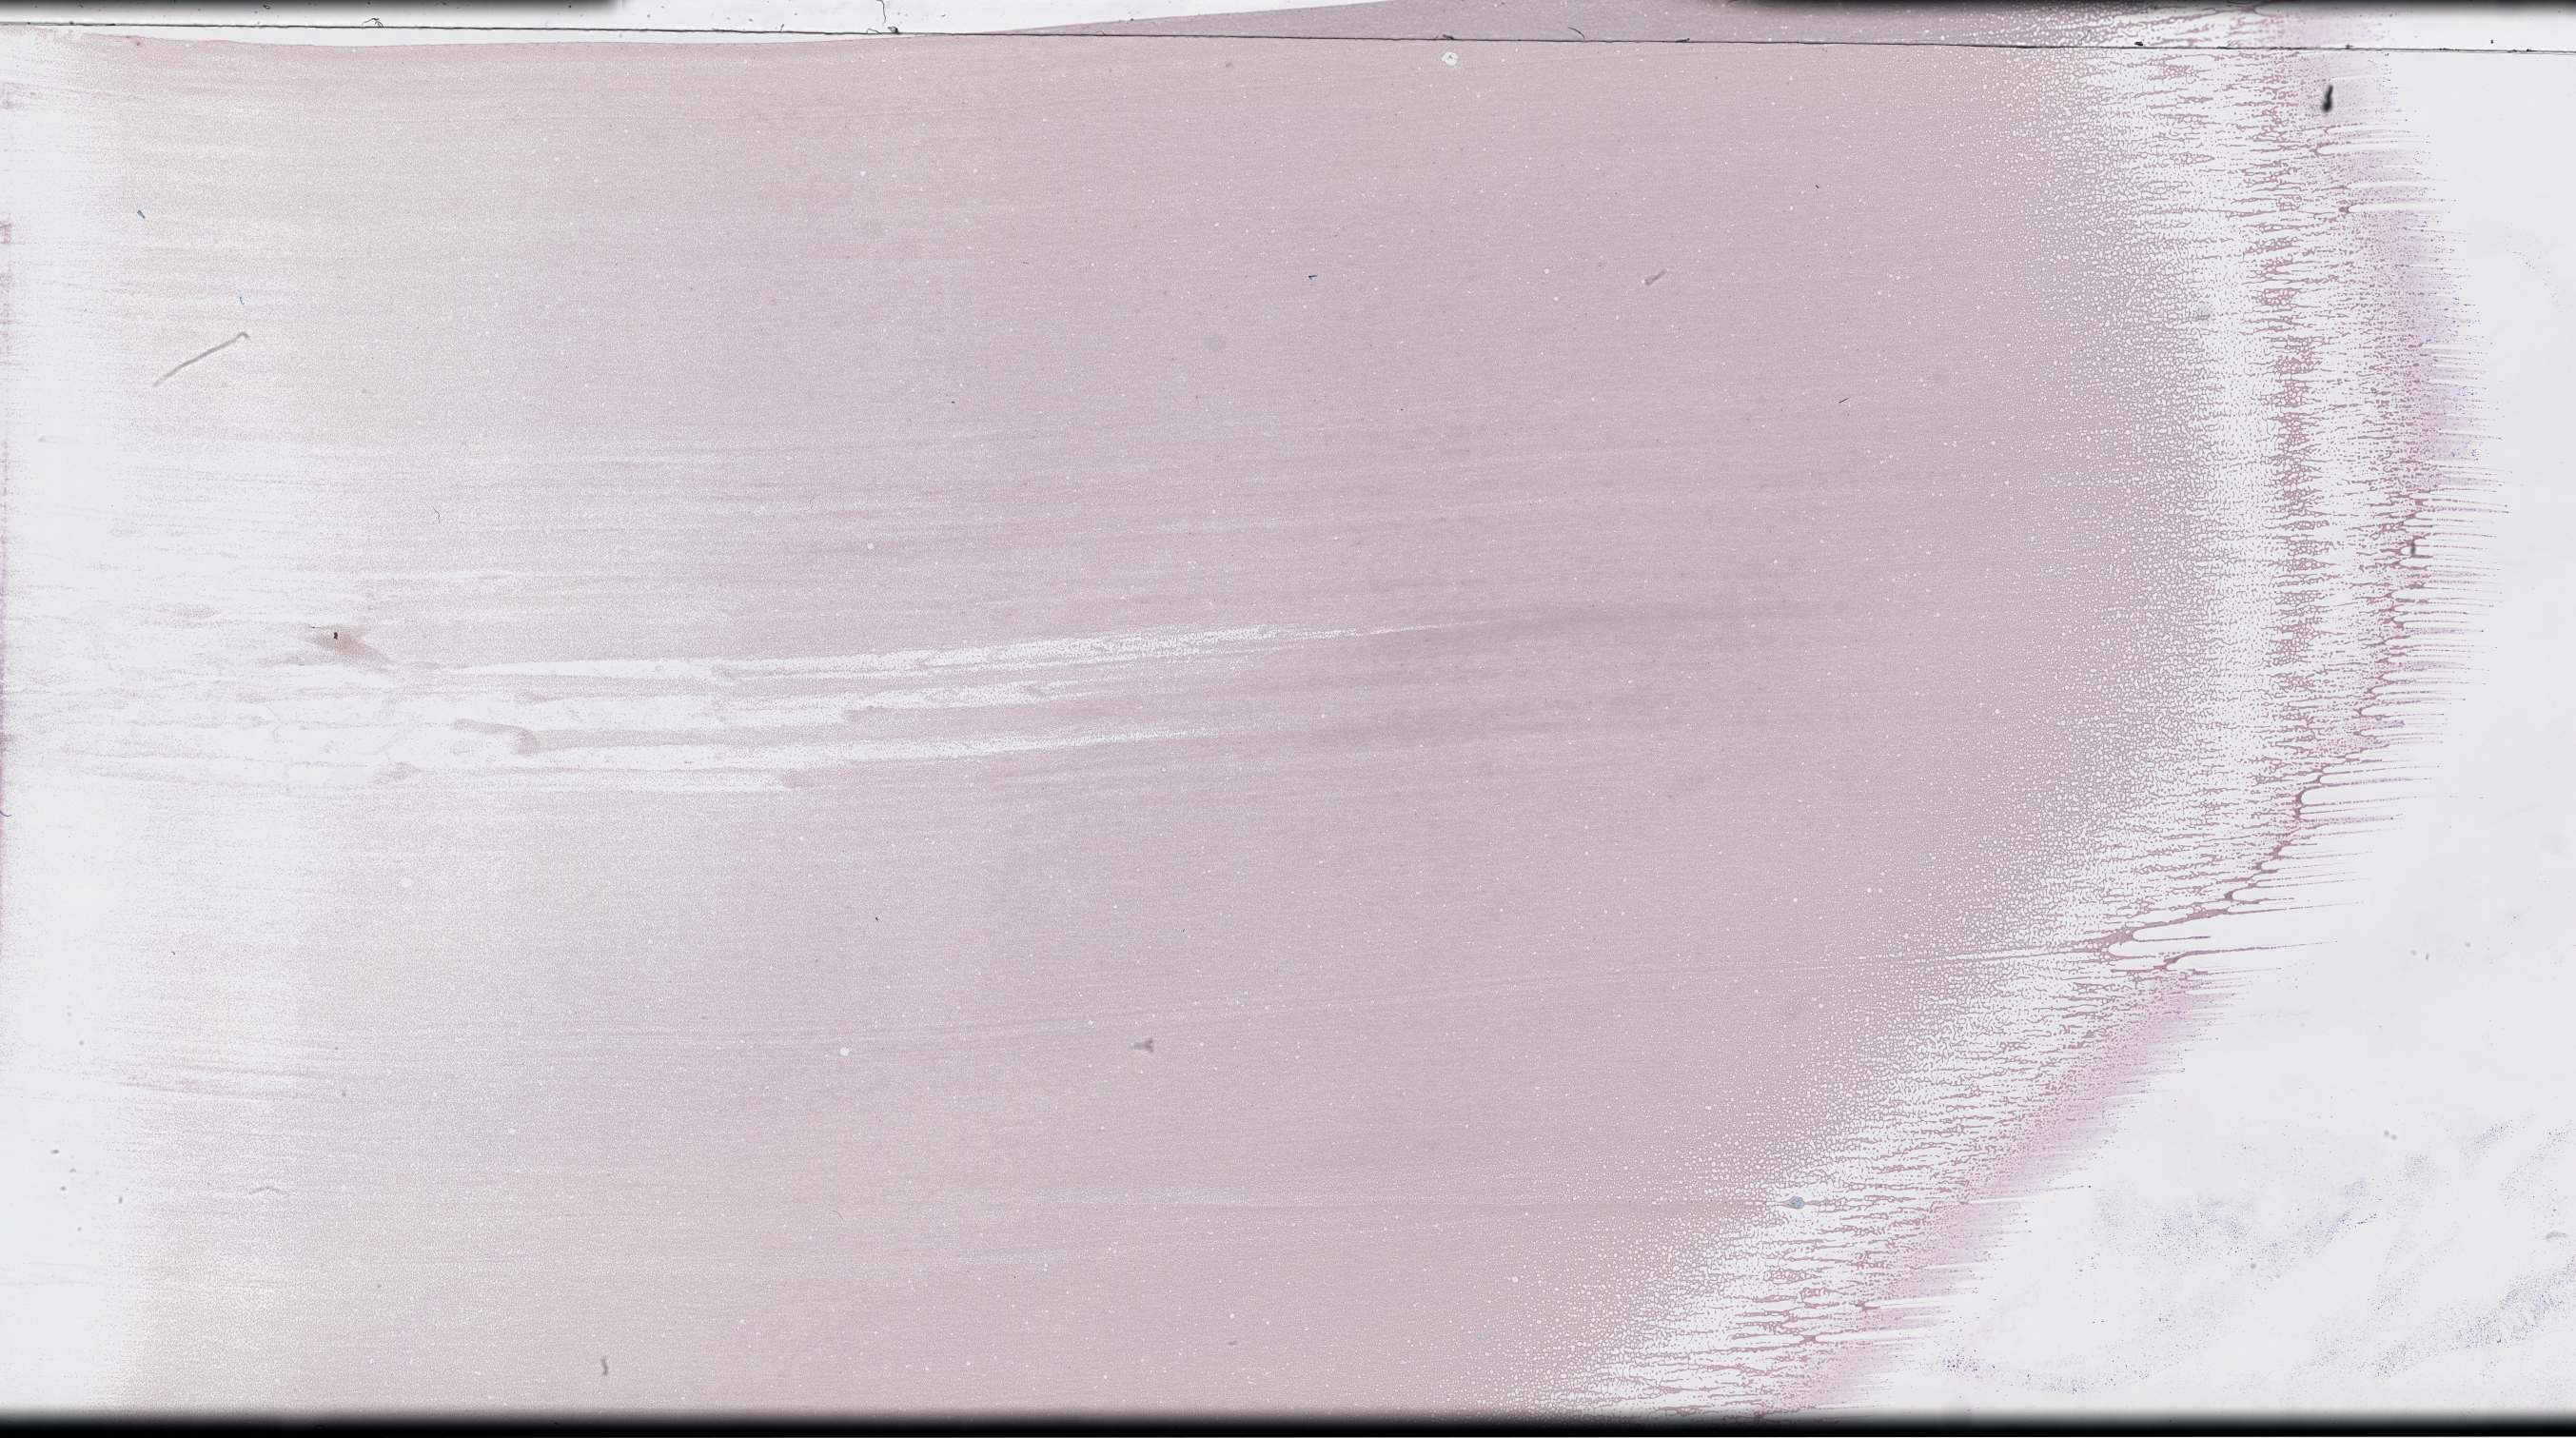
Wright-Giemsa-stained whole blood smear, whole-slide image, whole scanned area (about 43.7 x 24.4 mm) shown as a low-resolution overview. Smear from an EDTA sample. Specimen time point: collected on treatment. Patient sex: male.
Patient diagnosis: Plasma Cell Myeloma.